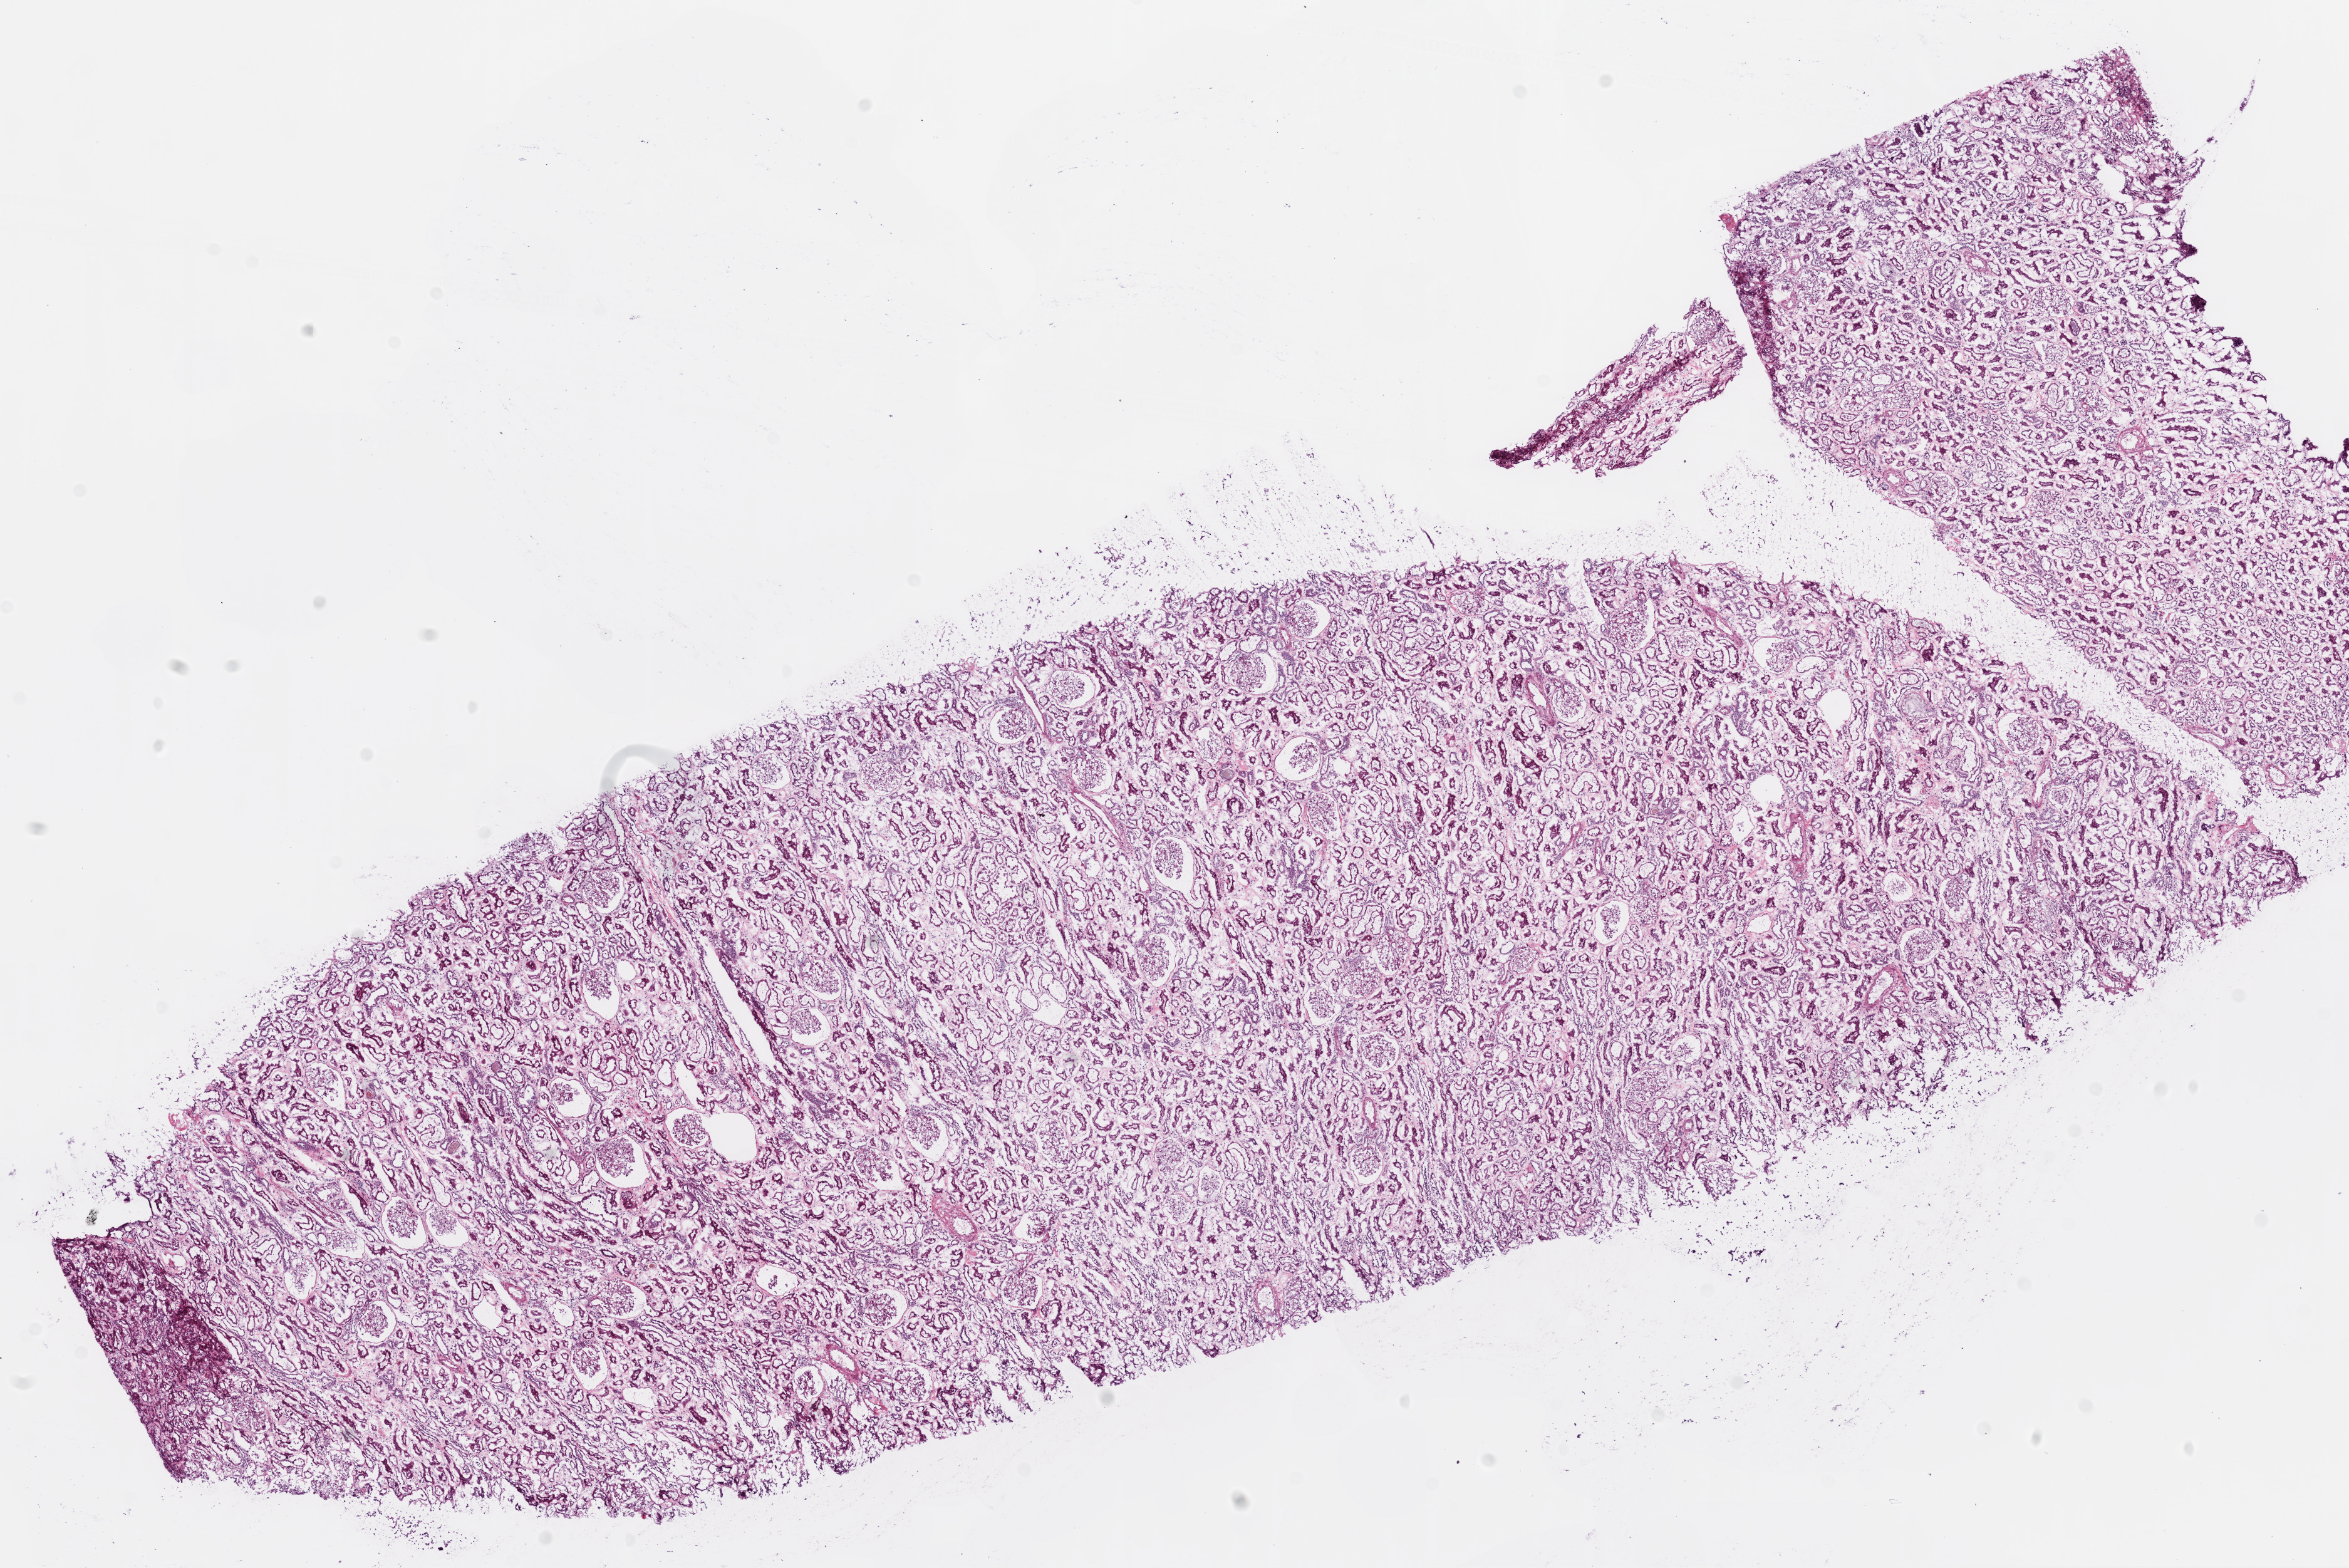
Whole-slide histology image, H&E, shown as a low-resolution overview of the whole scanned area (about 15.0 x 10.0 mm), frozen section, solid tissue normal (non-tumour tissue) sample from the kidney. Male, age 62 years at initial diagnosis.
This section: solid tissue normal (non-tumour) sample from the same patient. Patient diagnosis: Clear cell adenocarcinoma, NOS.